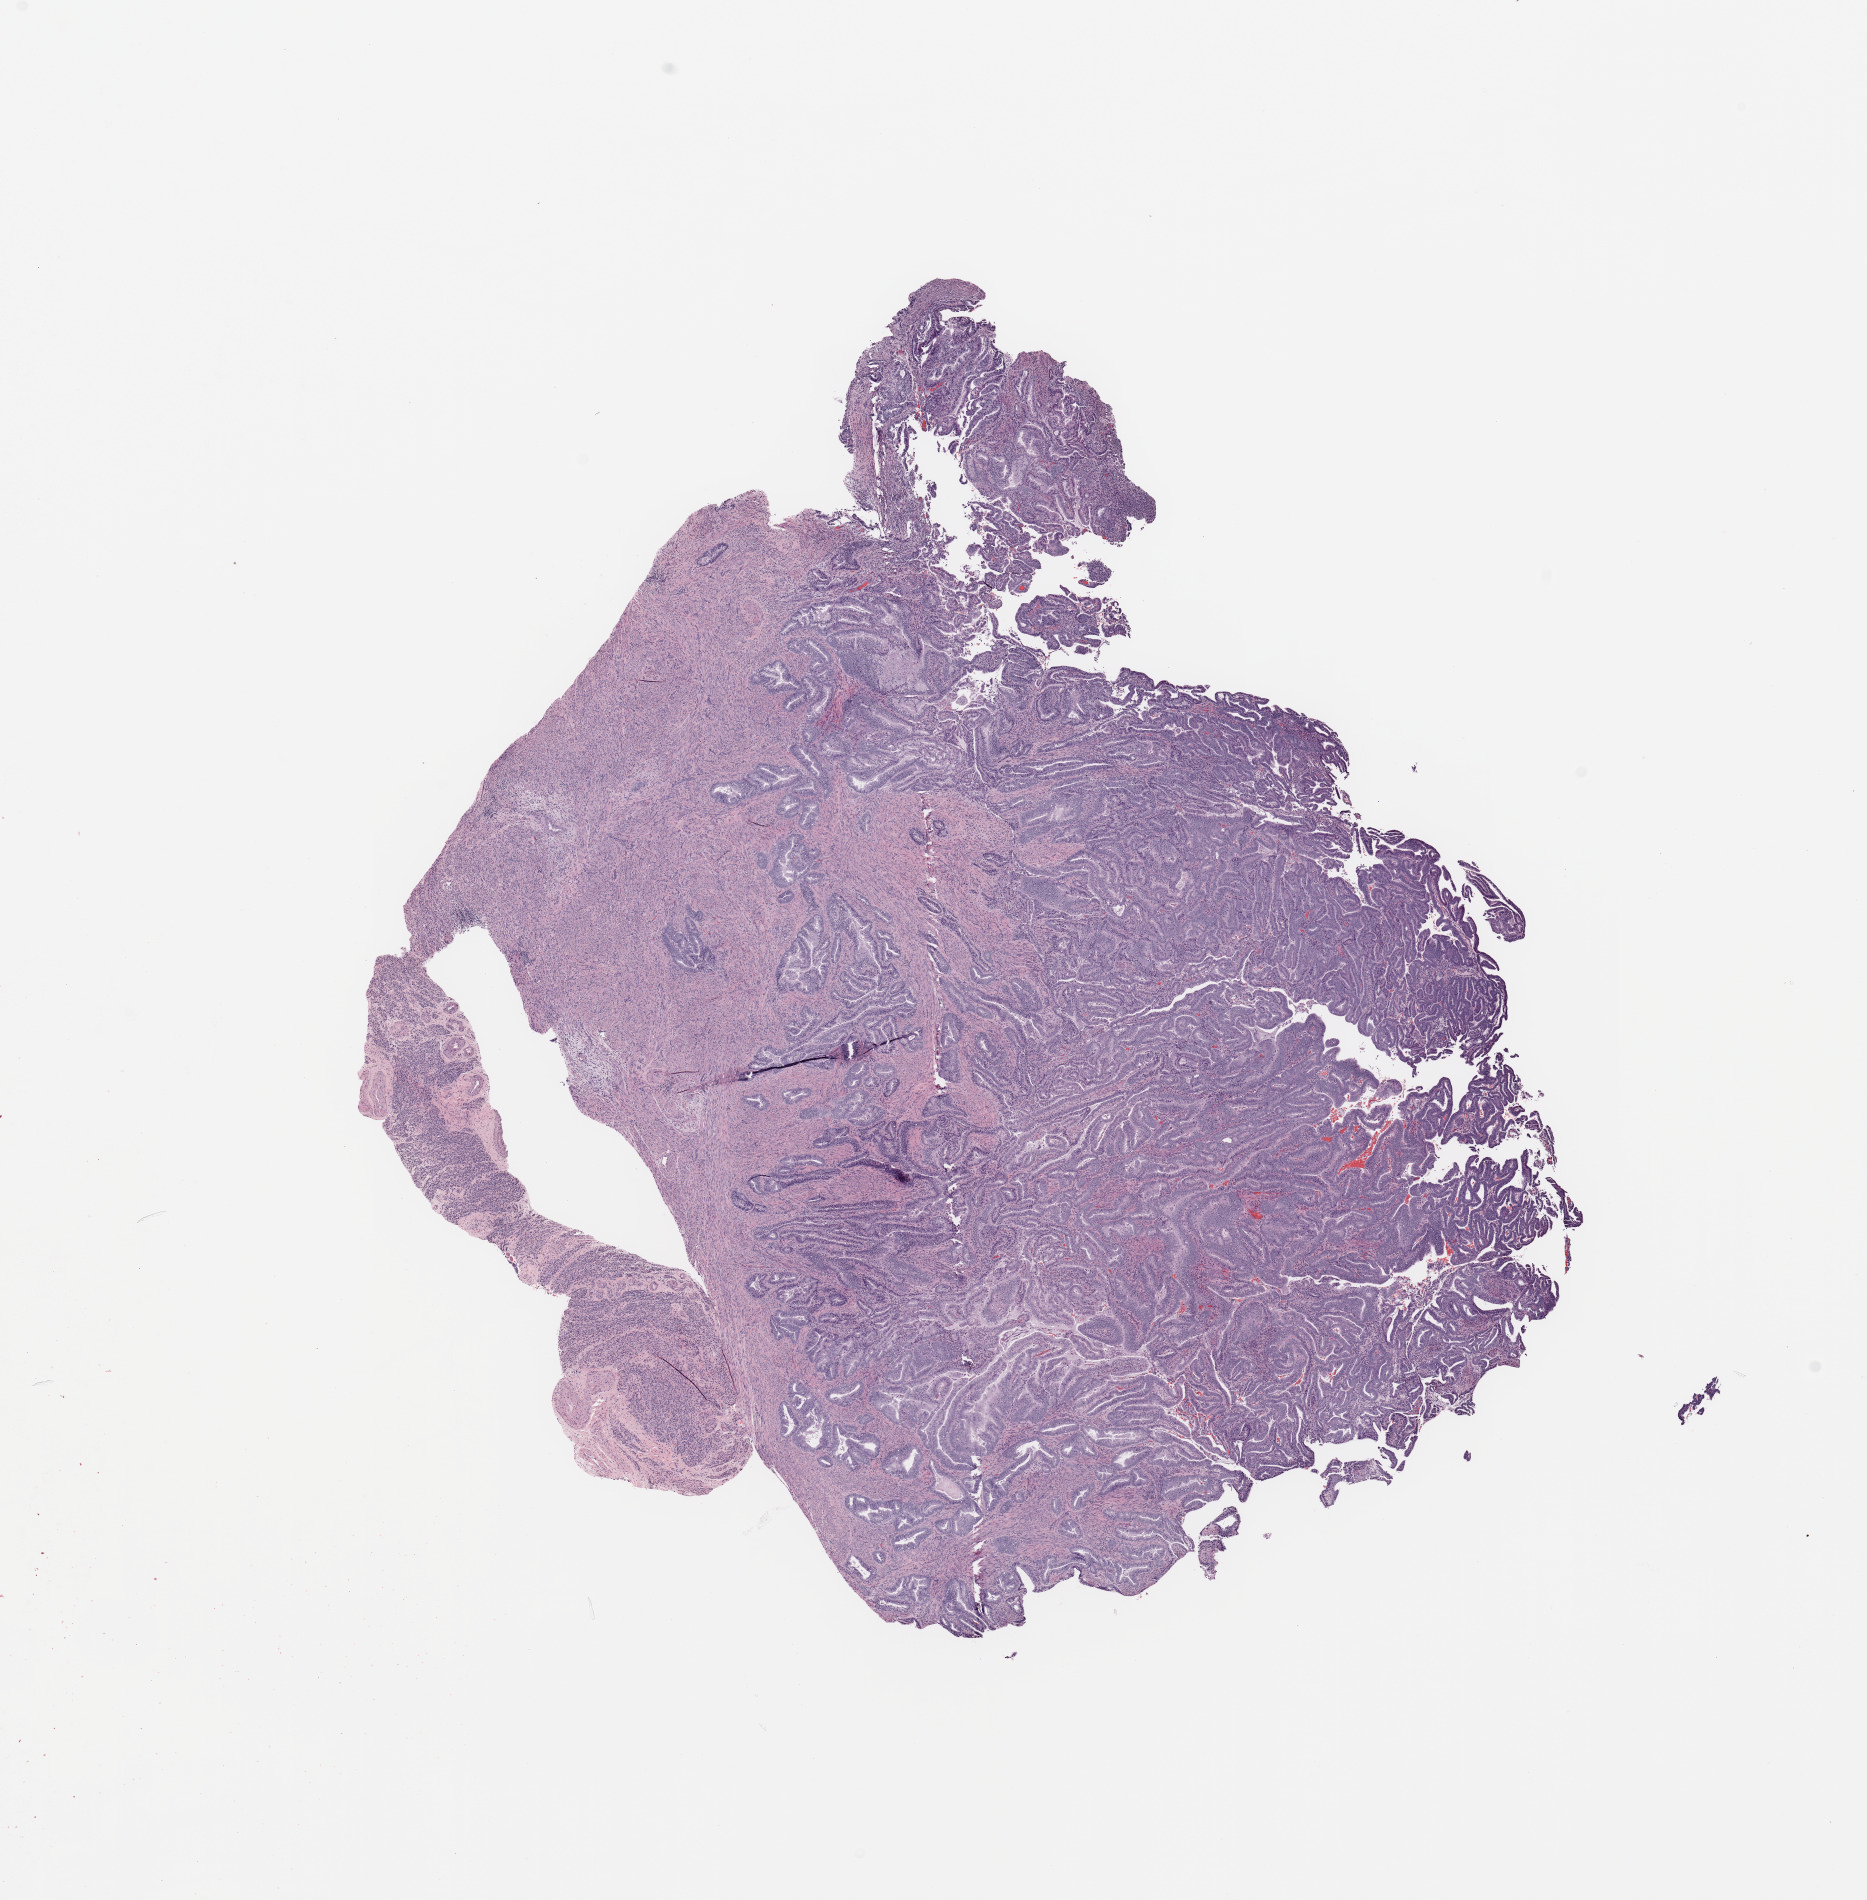
H&E-stained whole-slide image — a low-resolution overview of the entire scanned area, about 14.8 x 15.0 mm (from a 20x scan). Uterus, tumour tissue. Patient: female, age 70 years.
* patient diagnosis (cohort enrolment): corpus endometrial carcinoma (uterus)